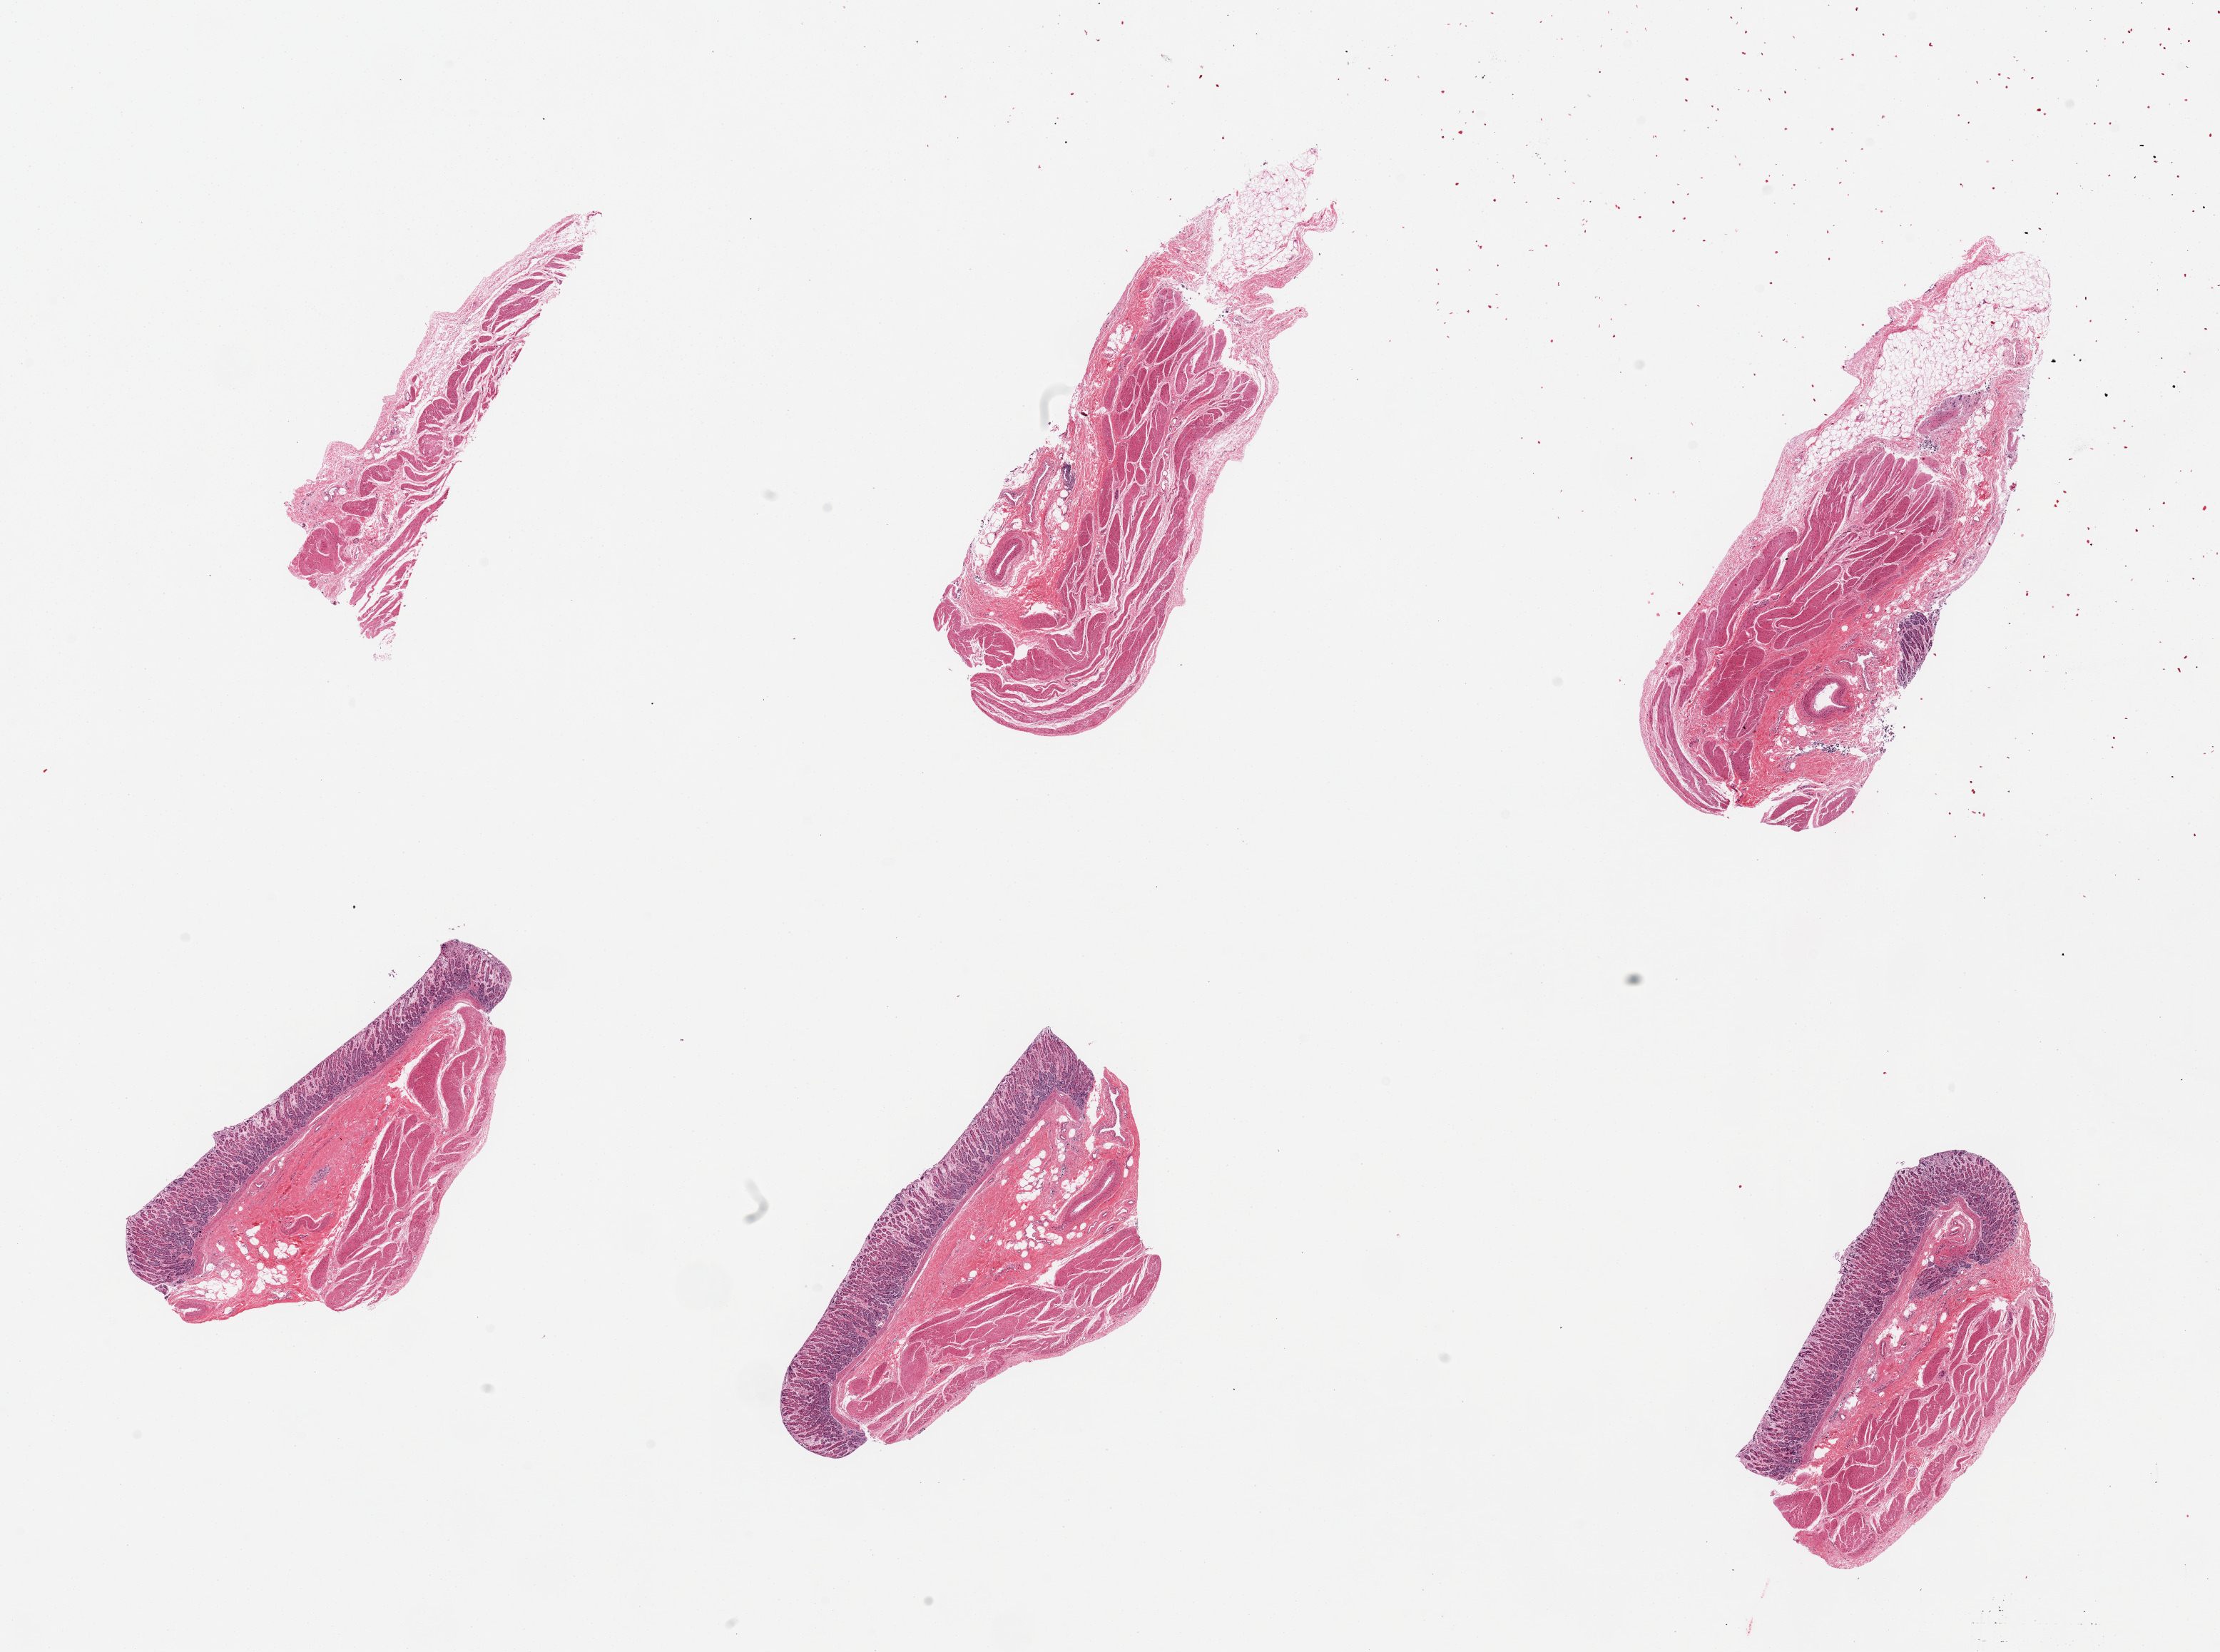
Digitized hematoxylin and eosin (H&E)-stained section — whole scanned area (about 24.6 x 18.3 mm, acquisition: 20x scan) shown as a low-resolution overview; PAXgene-fixed paraffin-embedded (PFPE) section; section of stomach (target tissue); donor tissue sample. Donor sex: female.
Reviewer comment on this tissue sample: 6 pieces, mucosa (moderately autolyzed) and muscularis.